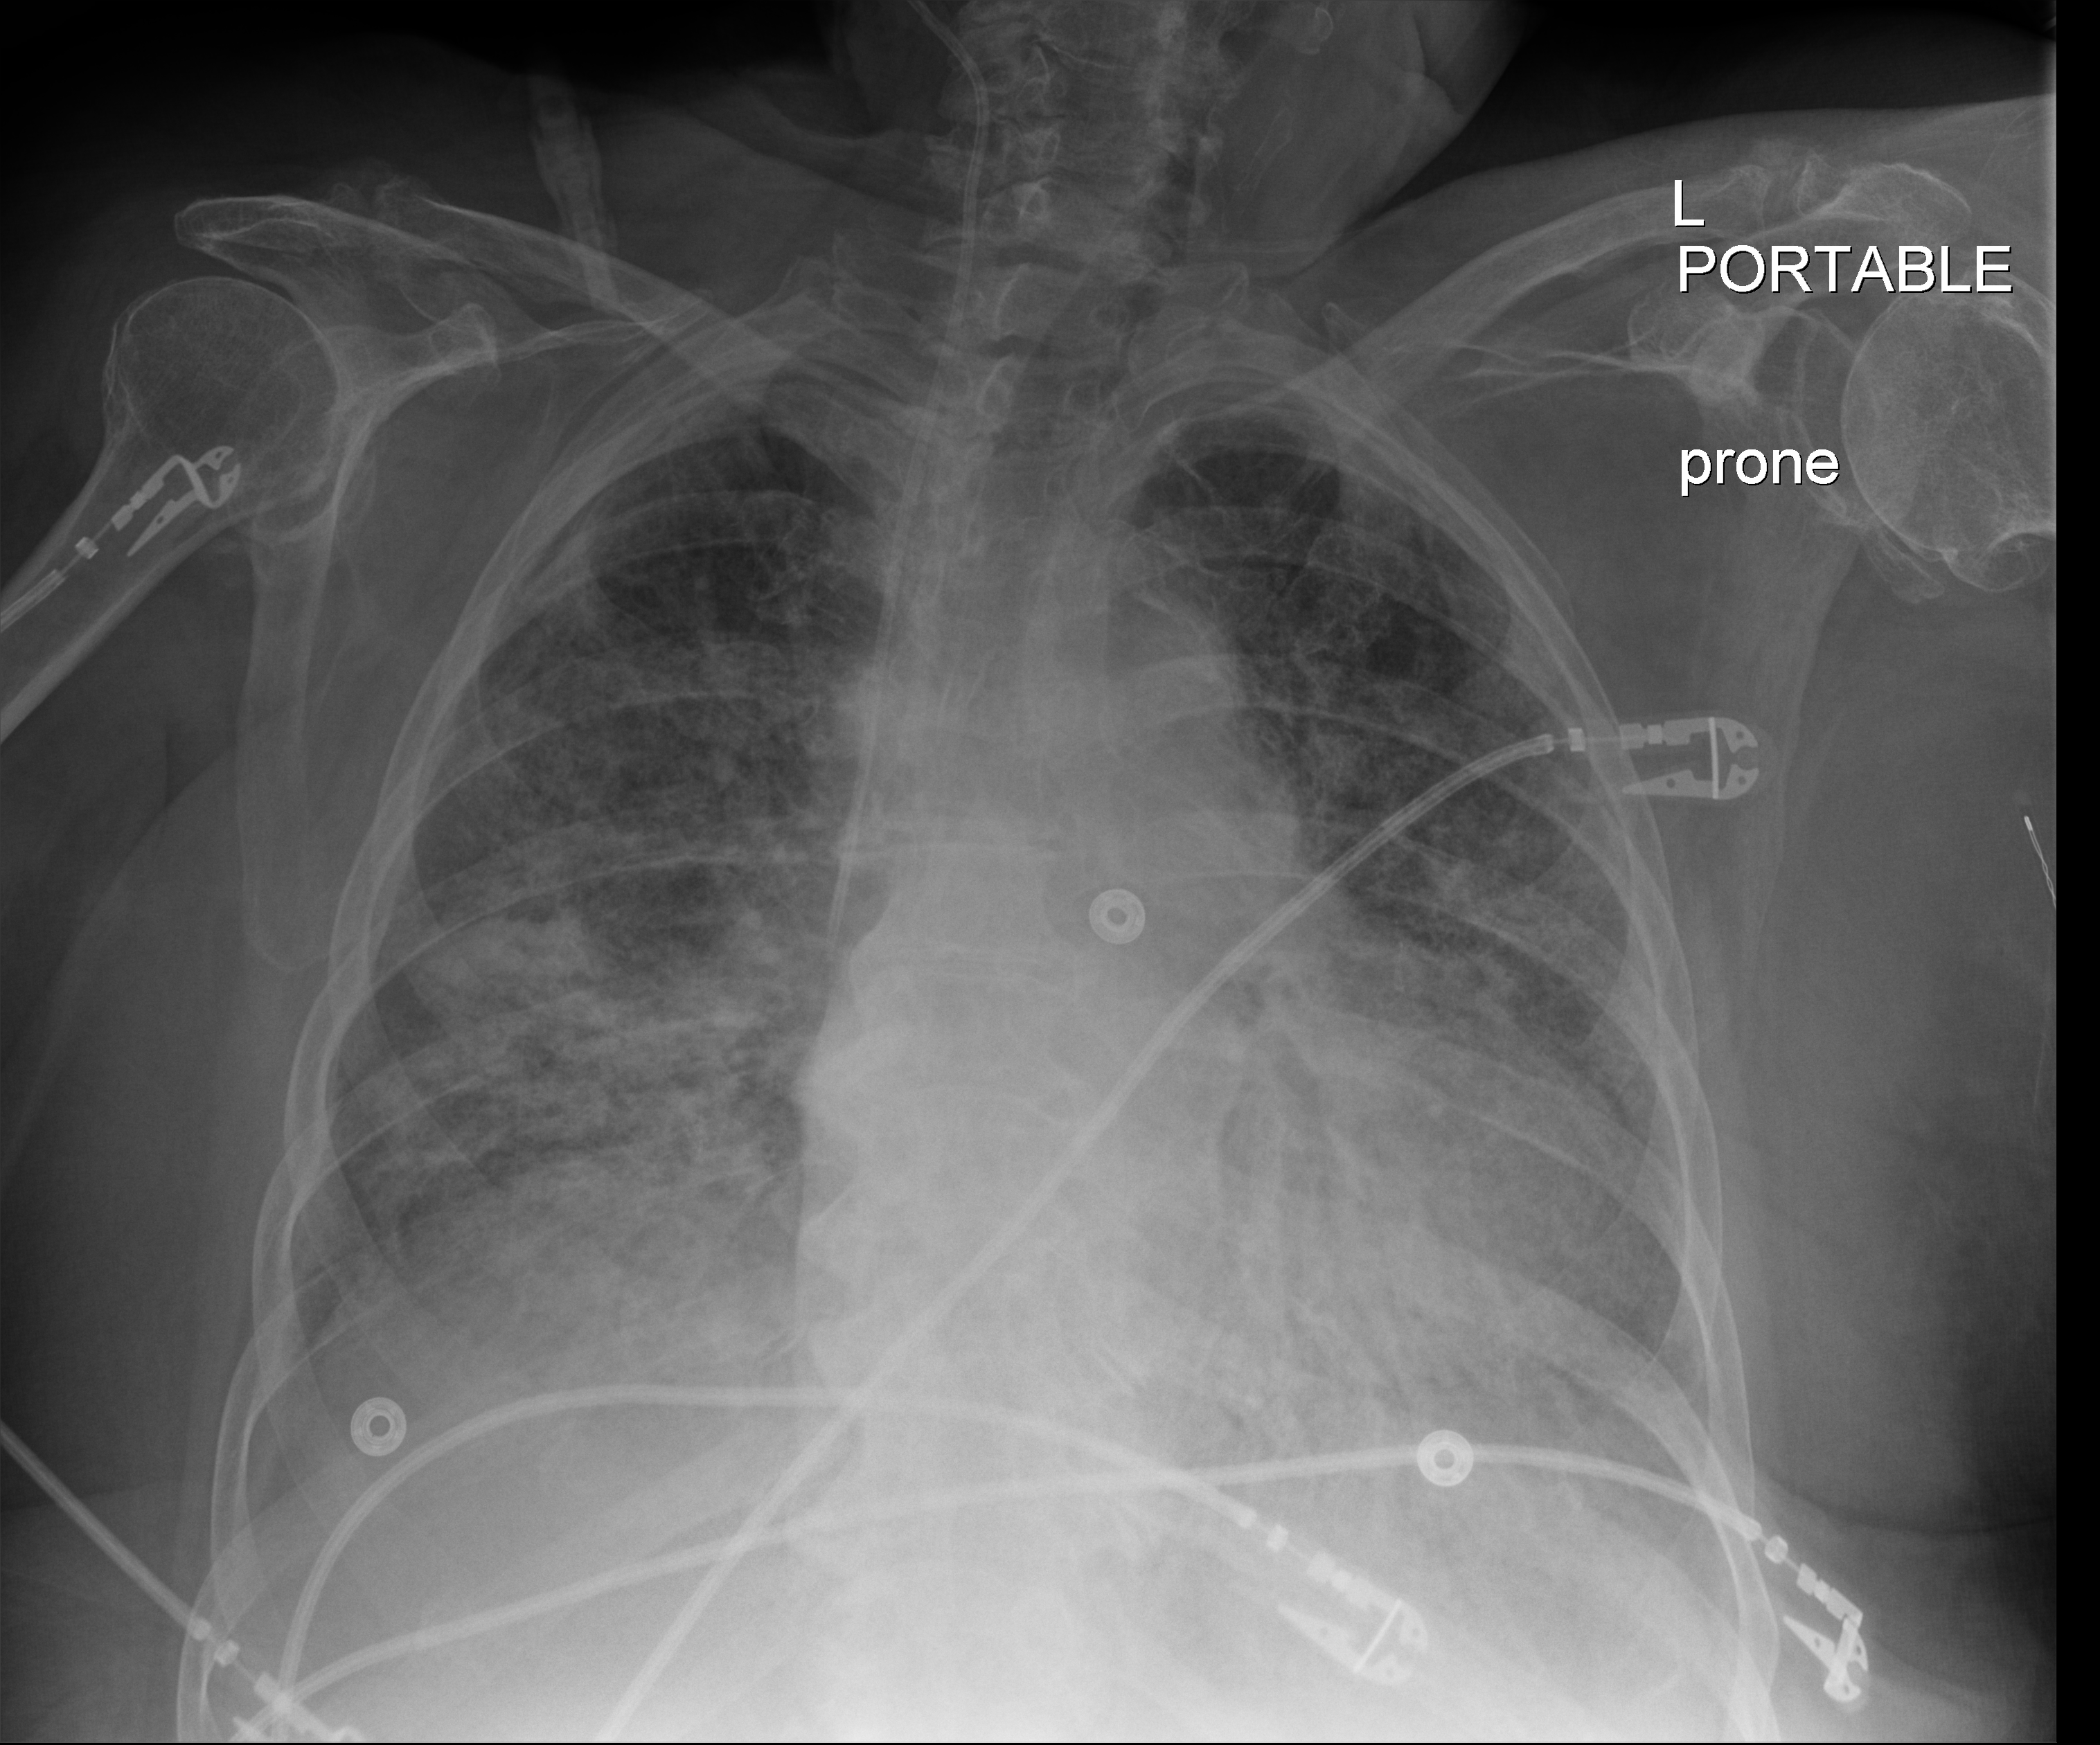
Chest X-ray (portable); anteroposterior (AP) projection. Patient hospitalised with COVID-19; female, aged 75–90 years.
Hospital-stay facts (about this admission, not read from this image; timing relative to this image not recorded): mechanically ventilated during this hospital stay: yes; hypertension (admission record): no; admitted to intensive care during this hospital stay: no.